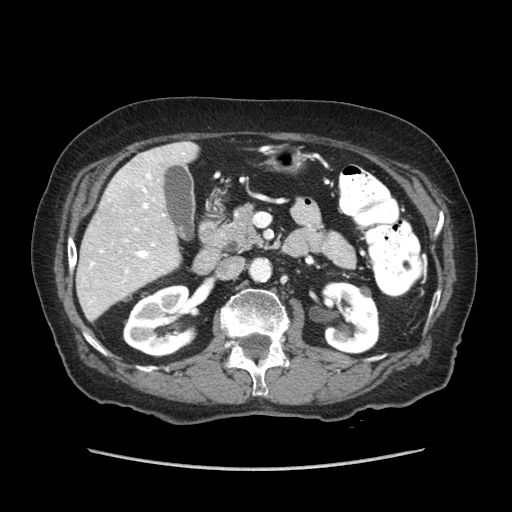
Contrast-enhanced abdominal CT (liver protocol), one axial slice; 140 kVp; soft-tissue window (W 400 / L 40 HU); 512 × 512 image matrix, field of view 360 × 360 mm. Case-level facts recorded for this patient, not image findings: diagnosis: hepatocellular carcinoma (patient treated with transarterial chemoembolisation; whether this scan precedes or follows treatment is not stated here); TNM stage (as recorded): Stage-IIIA; Child-Pugh class: A; tumour differentiation: well differentiated; tumour nodularity: multinodular.
Structures marked on this image (semi-automatically segmented with operator editing):
- liver parenchyma outside the tumour (the mass and vessels are separate outlines, so this box may not span the whole liver): bounding box [x1, y1, x2, y2] px = [76, 142, 198, 320]
- mass: [105, 157, 155, 209]
- liver vessels: [89, 152, 185, 303]